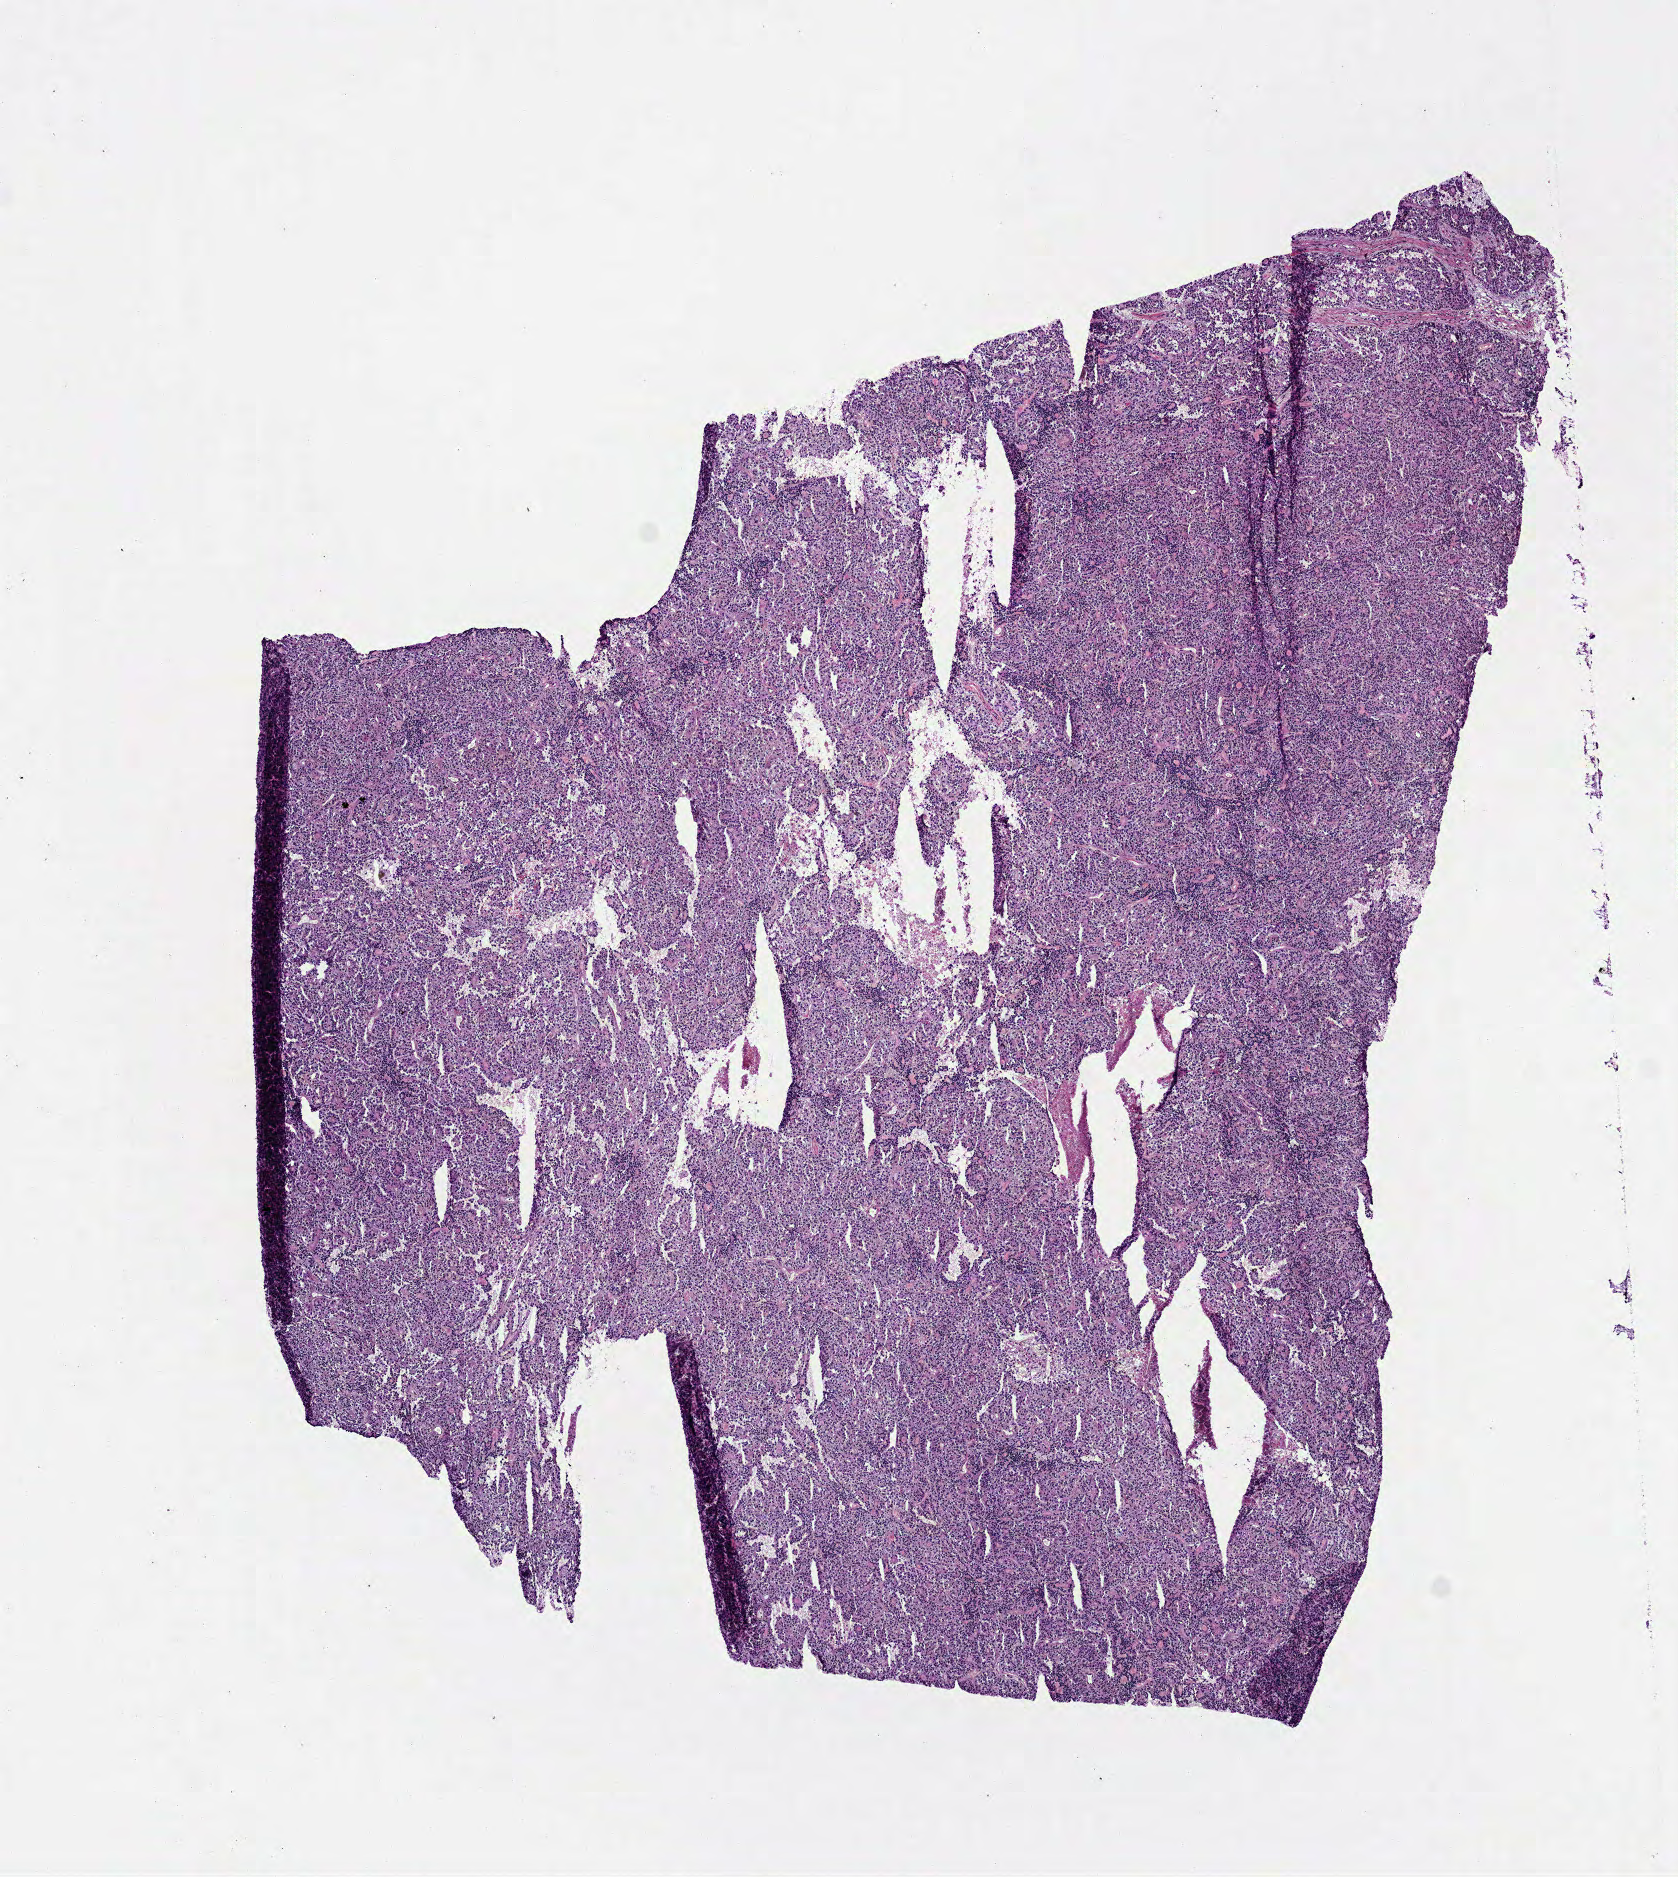
Hematoxylin and eosin (H&E) stained whole-slide image, shown as a low-resolution overview of the whole scanned area (about 6.8 x 7.6 mm, slide scanned at 40x), frozen section from the top of the tissue portion, sample: primary tumour, kidney. Male, age 58 years at initial diagnosis. Pathologist review of this section (percent, as recorded): tumour cells 95%, tumour nuclei 85%, normal cells 0%, stromal cells 5%, necrosis 0%.
Diagnosis: Papillary adenocarcinoma, NOS. Laterality: left. AJCC pathologic stage: I (7th edition).